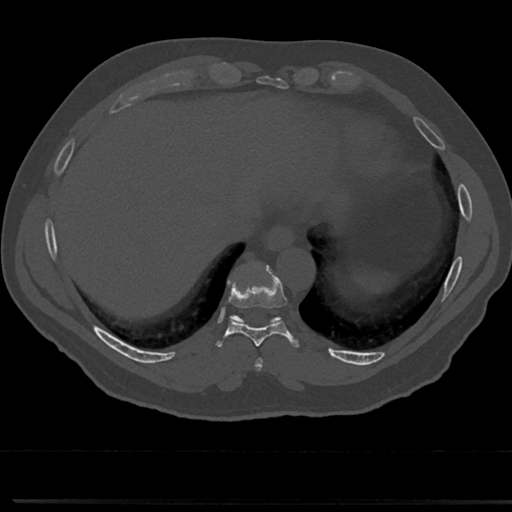
CT including the spine, one axial slice. Slice 296 of 817 in the series (ordered by position). 120 kVp. Bone window (W 1800 / L 400 HU). 512 × 512 image matrix, field of view 355 × 355 mm. Patient: male, 61 years. From the clinical record (not read from this slice): primary cancer: prostate.
Structures marked on this image (semi-automatically segmented with operator editing):
- T8 vertebra: bounding box (x1, y1, x2, y2) in pixels: (244, 328, 279, 358)
- T9 vertebra: (231, 266, 284, 331)